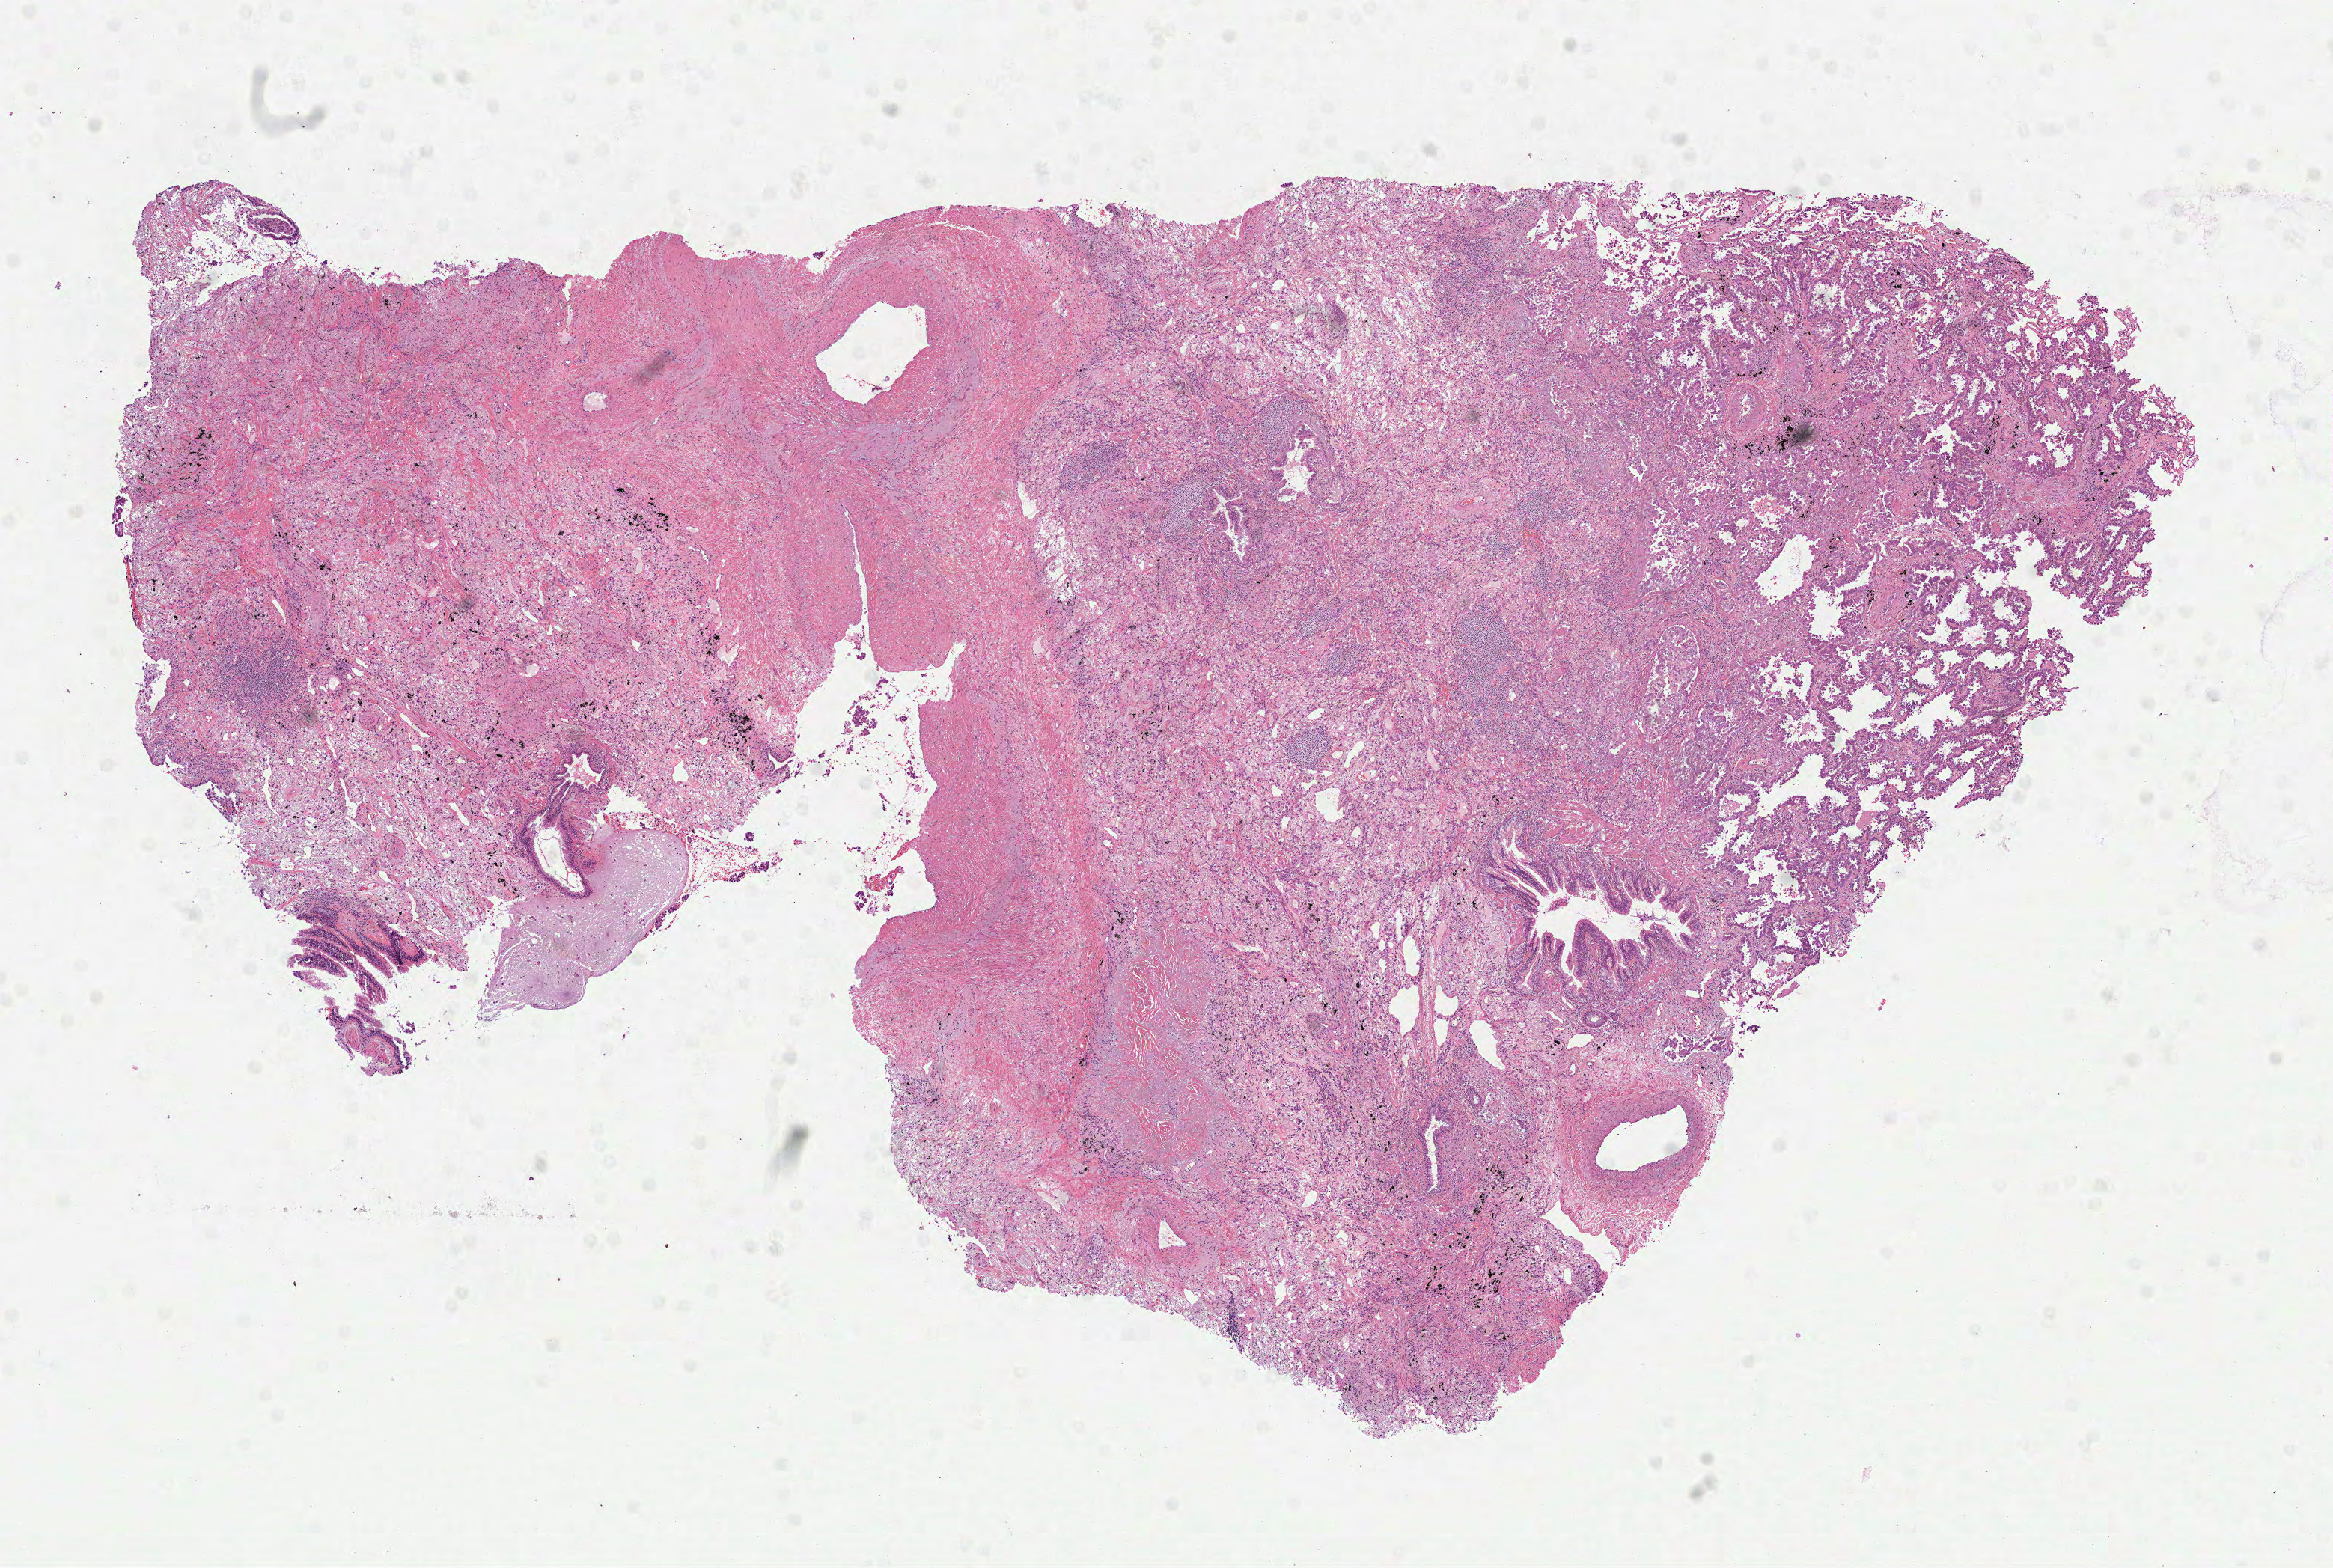
Whole-slide histology image, H&E, shown as a low-resolution overview of the whole scanned area (about 12.6 x 8.4 mm); formalin-fixed paraffin-embedded (FFPE) diagnostic section; sample: primary tumour, lung. Female patient; age at initial diagnosis 76 years.
- AJCC pathologic stage: IIIA (7th edition)
- pathologic diagnosis: Bronchiolo-alveolar carcinoma, non-mucinous (upper lobe, lung)